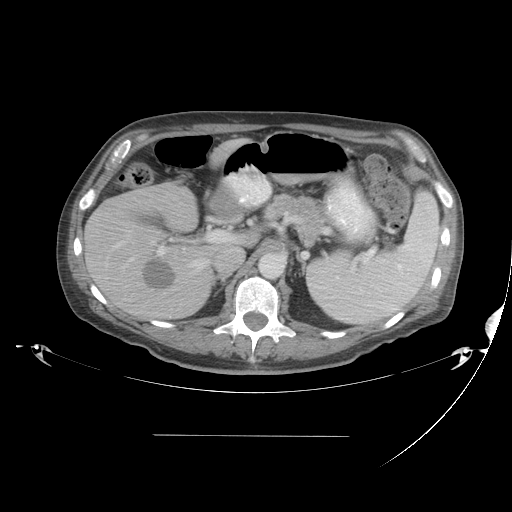
Contrast-enhanced abdominal CT, one axial slice. Slice 26 of 48 in the series (ordered by position). 120 kVp. Intravenous contrast given. Soft-tissue window (W 400 / L 40 HU). 5 mm slice thickness. 512 × 512 image matrix. Male patient, age 65 years. From the clinical record (not read from this slice): diagnosis: colorectal cancer liver metastases, imaged before liver resection.
Structures marked on this image (expert manual segmentation):
- hepatic veins: bounding box [x1, y1, x2, y2] px = [104, 230, 209, 301]
- liver: [86, 141, 238, 320]
- planned liver remnant (the part of the liver to remain after resection): [144, 141, 238, 221]
- portal vein (with intrahepatic branches): [150, 226, 234, 255]
- liver metastasis: [138, 258, 177, 290]